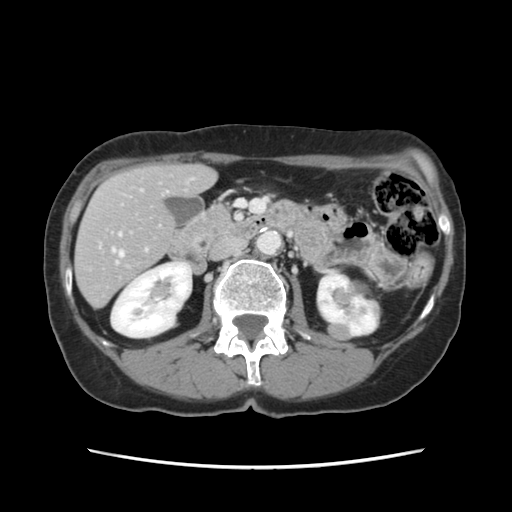
Contrast-enhanced abdominal CT, one axial slice. Position 48 of 120 along the scan axis. 120 kVp. Intravenous contrast given. Soft-tissue window (W 400 / L 40 HU). 512 × 512 image matrix, field of view 330 × 330 mm. Female patient, age 70 years. Case-level facts recorded for this patient, not image findings: diagnosis: colorectal cancer liver metastases, imaged before liver resection.
Structures marked on this image (manually delineated by an expert):
- hepatic veins: box from (x=112, y=249) to (x=124, y=257) px
- liver: (x=76, y=166)–(x=214, y=306)
- planned liver remnant (the part of the liver to remain after resection): (x=76, y=166)–(x=214, y=307)
- portal vein (with intrahepatic branches): (x=119, y=233)–(x=147, y=252)